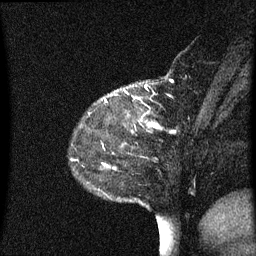
Breast MRI (dynamic contrast-enhanced), one sagittal slice; position 16 of 60 along the scan axis; dynamic contrast-enhanced series, image 2 of 3 at this slice position (ordered by acquisition); 1.5 T; TE 4.2 ms, TR 8.4 ms; 2 mm slice thickness; 256 × 256 image matrix. Female patient, age 48 years. From the clinical record (not read from this slice): setting: breast cancer imaged before/during neoadjuvant chemotherapy; receptor status: HR-positive, HER2-negative.
Outlined on this slice (semi-automatically segmented with operator editing):
- analysis volume of interest (the breast-tissue region the enhancement analysis was run in; not a lesion): box from (x=80, y=83) to (x=195, y=221) px
- tumour enhancement mask (voxels above the 70 % enhancement threshold inside the analysis volume of interest): (x=106, y=101)–(x=155, y=128)